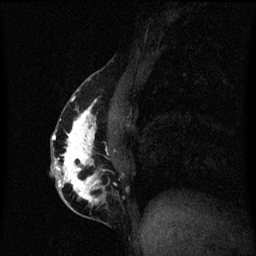
Breast MRI (dynamic contrast-enhanced), one sagittal slice; slice 26 of 60 in the series (ordered by position); dynamic contrast-enhanced series, image 2 of 3 at this slice position (ordered by acquisition); 1.5 T; TE 4.2 ms, TR 8.4 ms; 2 mm slice thickness; 256 × 256 image matrix, field of view 200 × 200 mm. Patient: female, 40 years.
Annotated regions visible in this slice (semi-automatic segmentation, software-assisted and operator-edited):
- analysis volume of interest (the breast-tissue region the enhancement analysis was run in; not a lesion): bounding box <51,84,118,211> (left, top, right, bottom; pixels)
- tumour enhancement mask (voxels above the 70 % enhancement threshold inside the analysis volume of interest): <53,92,103,205>